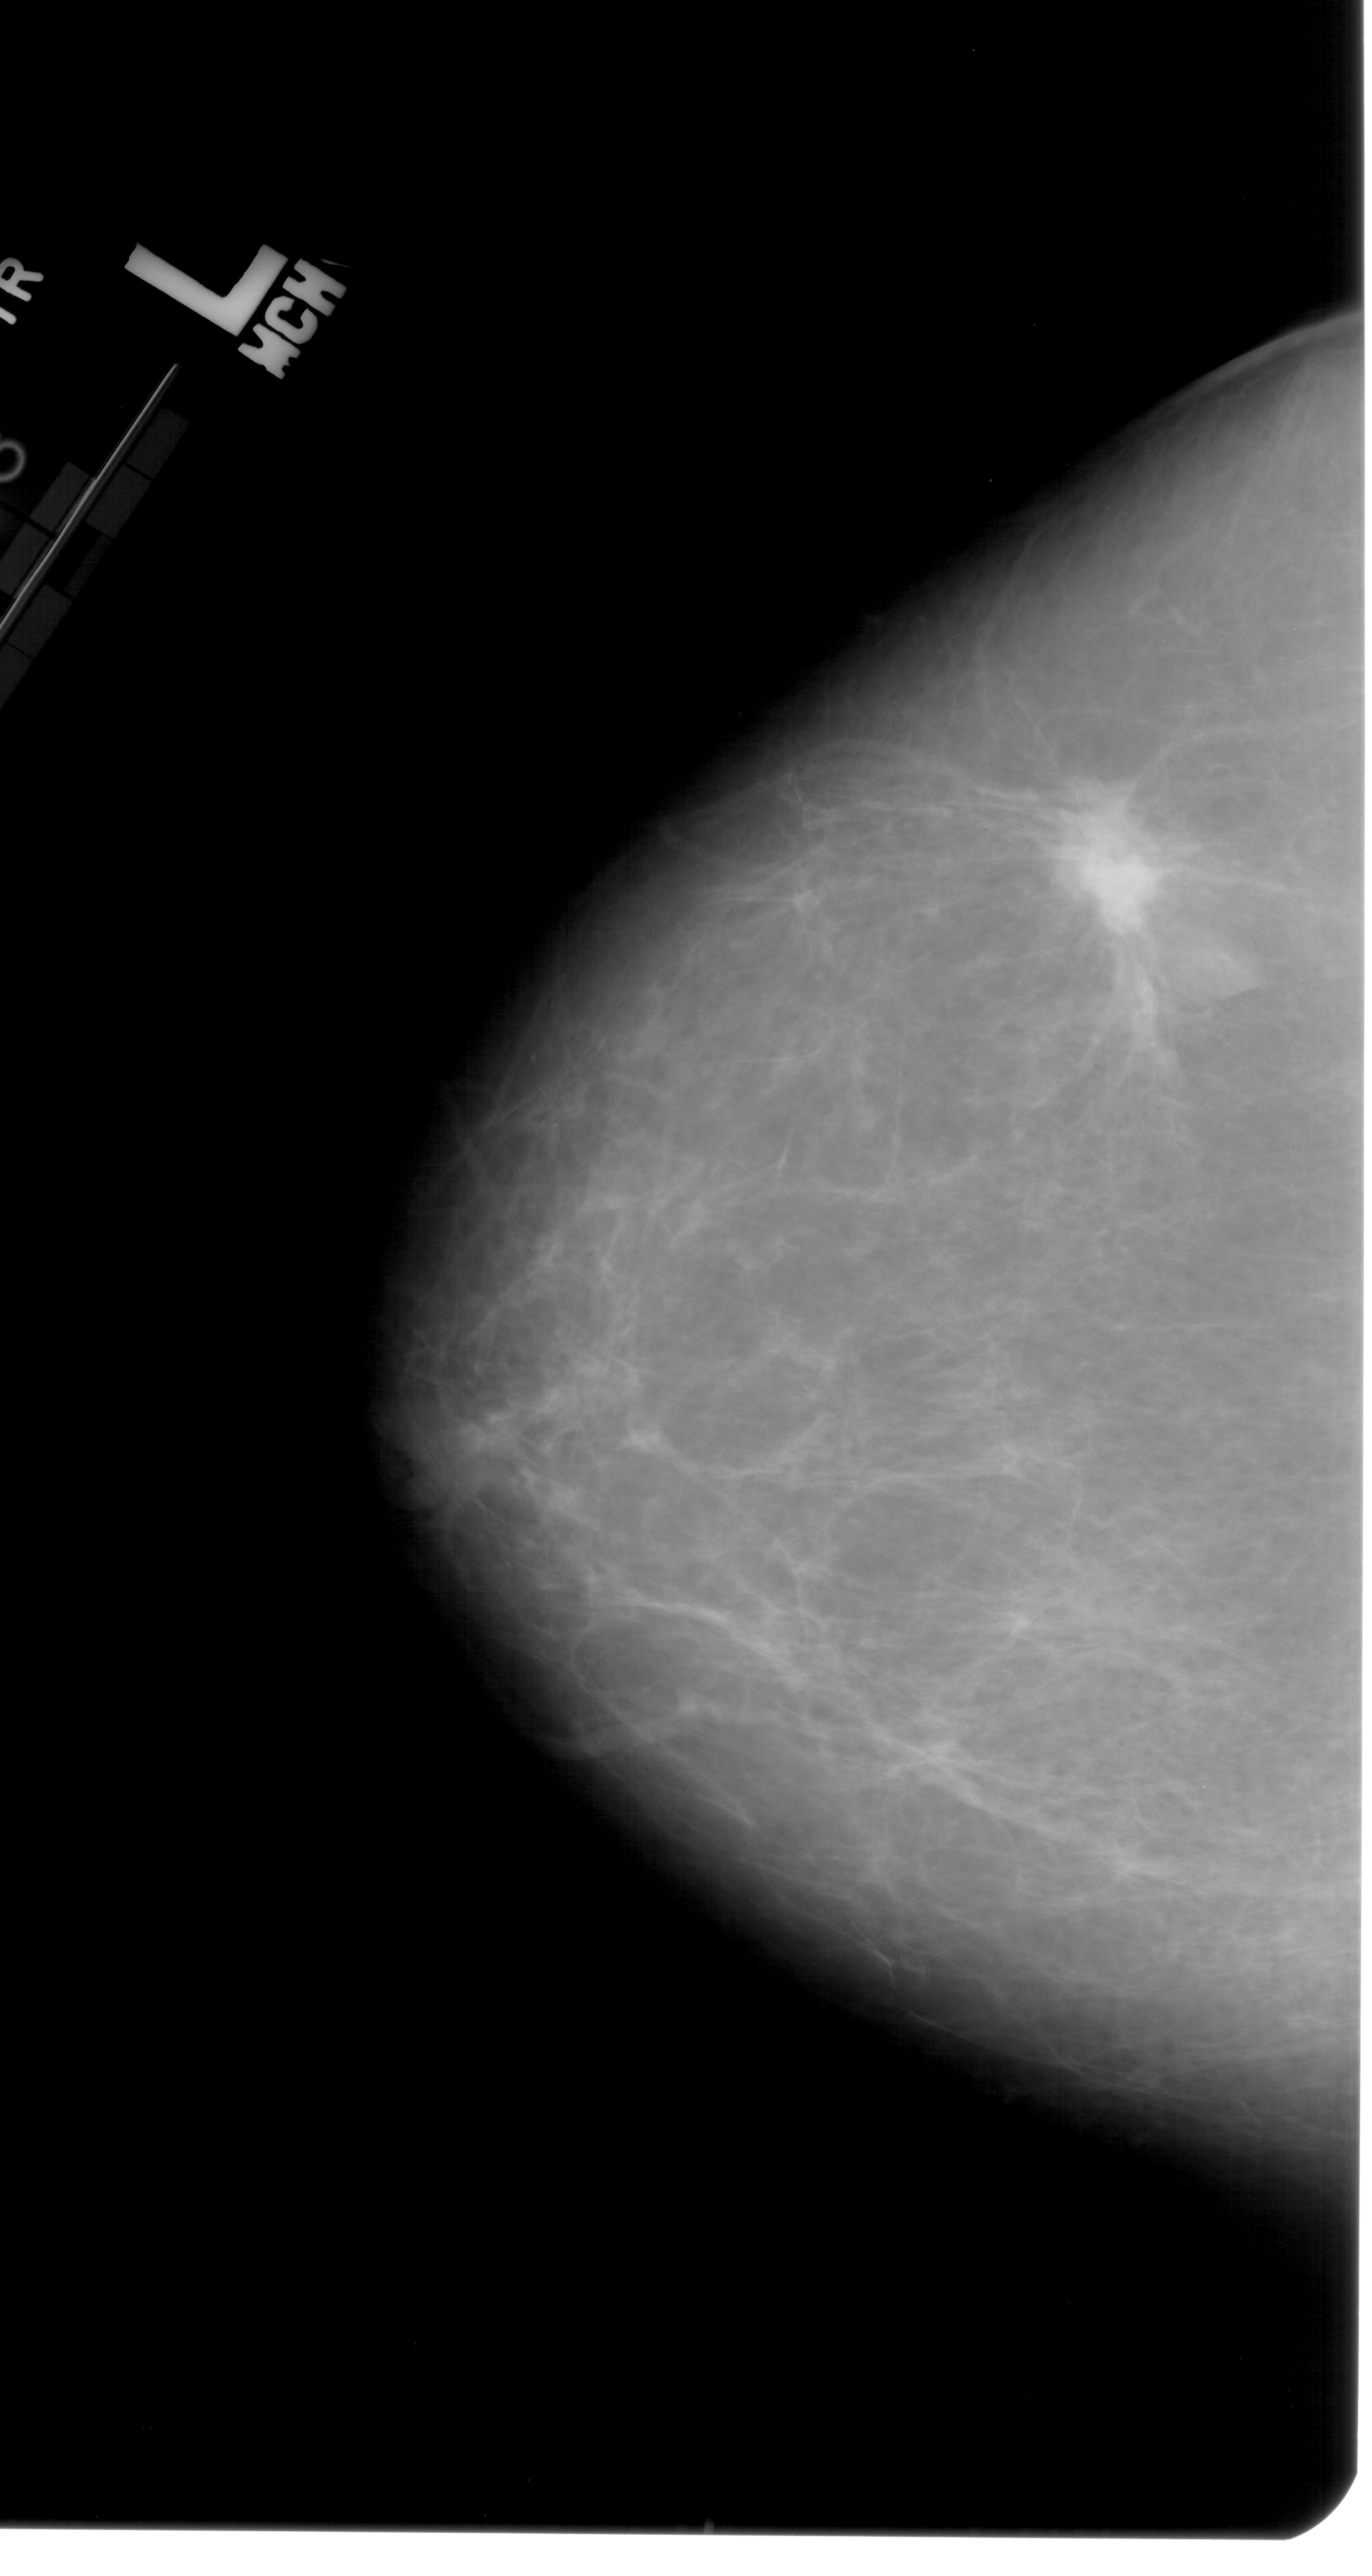
Digitized screen-film mammogram, left breast, craniocaudal (CC) view, BI-RADS breast density category 2 (scale 1–4).
- Marked findings (only marked abnormalities are described; nothing is implied about the rest of the image): mass, shape irregular, margins spiculated; BI-RADS assessment category 5; subtlety rating 5 on a 1 (subtle) to 5 (obvious) scale; pathology (as recorded): malignant.